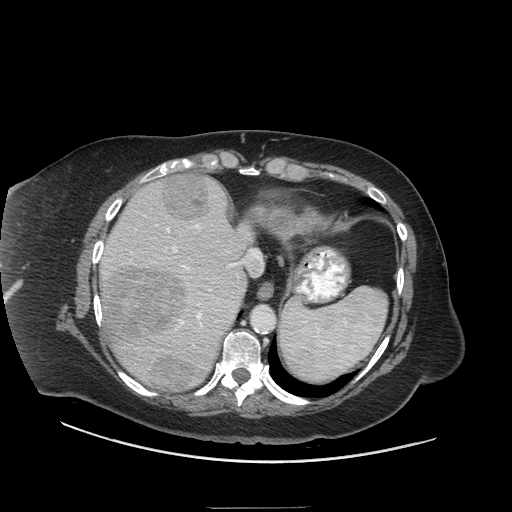
Contrast-enhanced abdominal CT (liver protocol), one axial slice. Slice 52 of 81 in the series (ordered by position). Reconstruction kernel STANDARD. Soft-tissue window (W 400 / L 40 HU). 2.5 mm slice thickness. 512 × 512 image matrix. Case-level facts recorded for this patient, not image findings: diagnosis: hepatocellular carcinoma (patient treated with transarterial chemoembolisation; whether this scan precedes or follows treatment is not stated here); TNM stage (as recorded): Stage-II; Child-Pugh class: A; tumour differentiation: moderately differentiated; tumour nodularity: multinodular.
Structures marked on this image (semi-automatically segmented with operator editing):
- liver parenchyma outside the tumour (the mass and vessels are separate outlines, so this box may not span the whole liver): bounding box [x1, y1, x2, y2] px = [100, 176, 264, 388]
- mass: [107, 174, 209, 391]
- liver vessels: [103, 195, 262, 352]